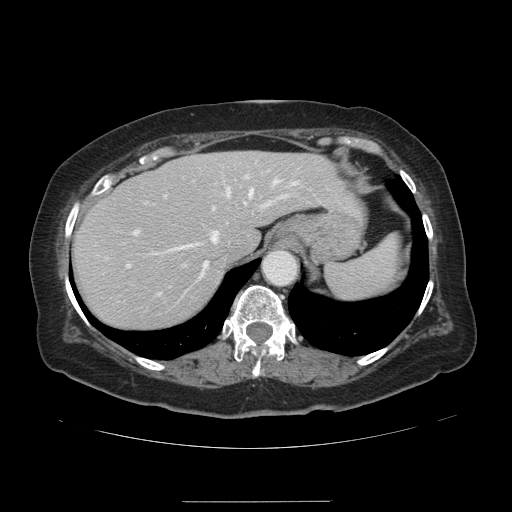
Contrast-enhanced abdominal CT, one axial slice; position 103 of 141 along the scan axis; intravenous contrast given; soft-tissue window (W 400 / L 40 HU); 512 × 512 image matrix. Female patient, age 74 years. From the clinical record (not read from this slice): diagnosis: colorectal cancer liver metastases, imaged before liver resection; multiple liver metastases: yes; largest metastasis: 7 cm; disease in both lobes: yes.
Structures marked on this image (manually delineated by an expert):
- hepatic veins: bounding box (x1, y1, x2, y2) in pixels: (104, 179, 296, 299)
- liver: (71, 151, 360, 331)
- planned liver remnant (the part of the liver to remain after resection): (71, 151, 360, 330)
- portal vein (with intrahepatic branches): (127, 174, 287, 295)